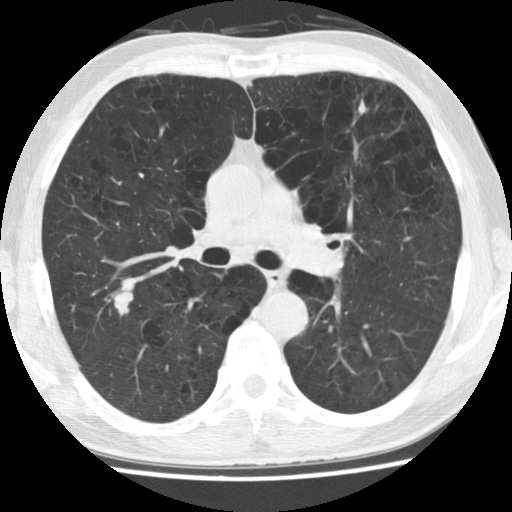
Low-dose screening chest CT, one axial slice; slice 92 of 158 in the series (ordered by position); reconstruction kernel STANDARD; lung window (W 1500 / L -600 HU); 512 × 512 image matrix.
Outlined on this slice (outlined manually by an expert reader):
- lesion 1 (tumor, upper lobe of right lung): bounding box <114,292,133,315> (left, top, right, bottom; pixels)